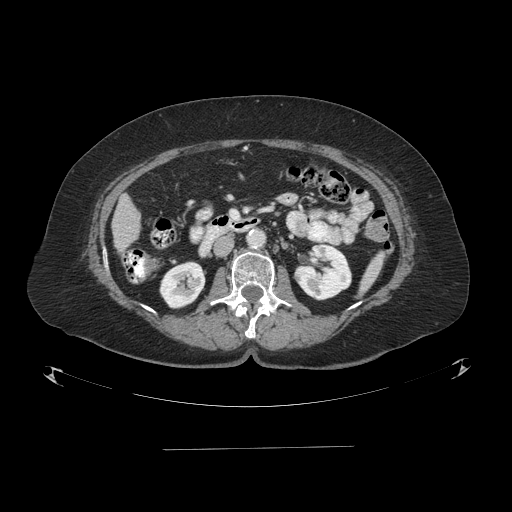
Contrast-enhanced abdominal CT (liver protocol), one axial slice; reconstruction kernel STANDARD; 120 kVp; one of 2 acquisitions stored at this slice position; soft-tissue window (W 400 / L 40 HU); 2.5 mm slice thickness; 512 × 512 image matrix, field of view 500 × 500 mm. From the clinical record (not read from this slice): diagnosis: hepatocellular carcinoma (patient treated with transarterial chemoembolisation; whether this scan precedes or follows treatment is not stated here); TNM stage (as recorded): Stage-IIIA; Child-Pugh class: A; tumour differentiation: poorly differentiated; tumour nodularity: multinodular.
Structures marked on this image (semi-automatically segmented with operator editing):
- liver parenchyma outside the tumour (the mass and vessels are separate outlines, so this box may not span the whole liver): bounding box (x1, y1, x2, y2) in pixels: (112, 194, 140, 258)